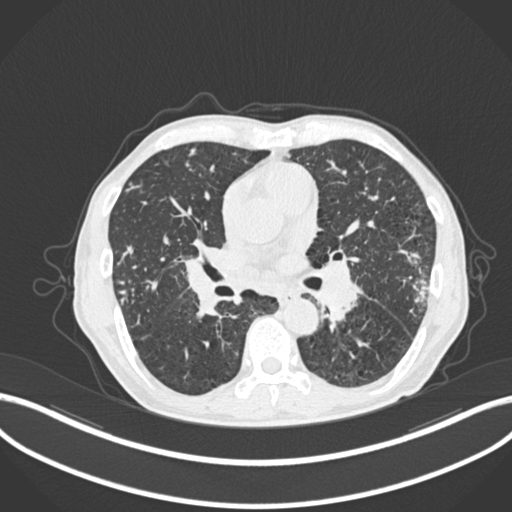
Chest CT, one axial slice; slice 119 of 287 in the series (ordered by position); reconstruction kernel B30f; 120 kVp; lung window (W 1500 / L -600 HU); 1 mm slice thickness; 512 × 512 image matrix, field of view 400 × 400 mm. Patient: male, 74 years. From the clinical record (not read from this slice): clinical TNM (as recorded): T2a N1 M0.
Structures marked on this image (bounding box drawn by a radiologist):
- lung tumour (recorded histology: adenocarcinoma): bounding box <402,248,426,271> (left, top, right, bottom; pixels)